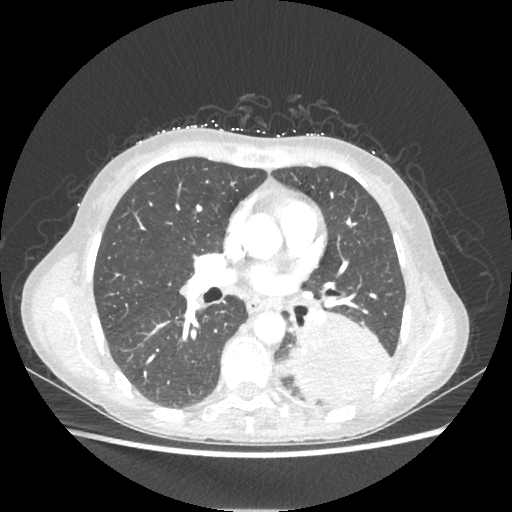
Chest CT, one axial slice. Position 117 of 221 along the scan axis. Reconstruction kernel STANDARD. 80 kVp. Lung window (W 1500 / L -600 HU). 1.25 mm slice thickness. 512 × 512 image matrix, field of view 360 × 360 mm. Female patient, age 53 years. From the clinical record (not read from this slice): clinical TNM (as recorded): T3 N0 M0.
Structures marked on this image (rectangle marked by the reading radiologist):
- lung tumour (recorded histology: adenocarcinoma): bounding box <286,305,389,403> (left, top, right, bottom; pixels)